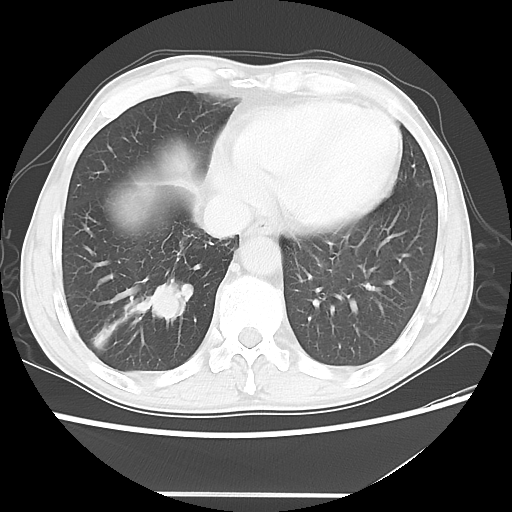
Chest CT, one axial slice. Position 14 of 56 along the scan axis. Reconstruction kernel LUNG. 120 kVp. Lung window (W 1500 / L -600 HU). 5 mm slice thickness. 512 × 512 image matrix. Patient: male, 65 years. From the clinical record (not read from this slice): clinical TNM (as recorded): T1c N3 M0; histopathological grade: G3.
Outlined on this slice (bounding box drawn by a radiologist):
- lung tumour (recorded histology: small cell carcinoma): bounding box [x1, y1, x2, y2] px = [139, 278, 204, 324]